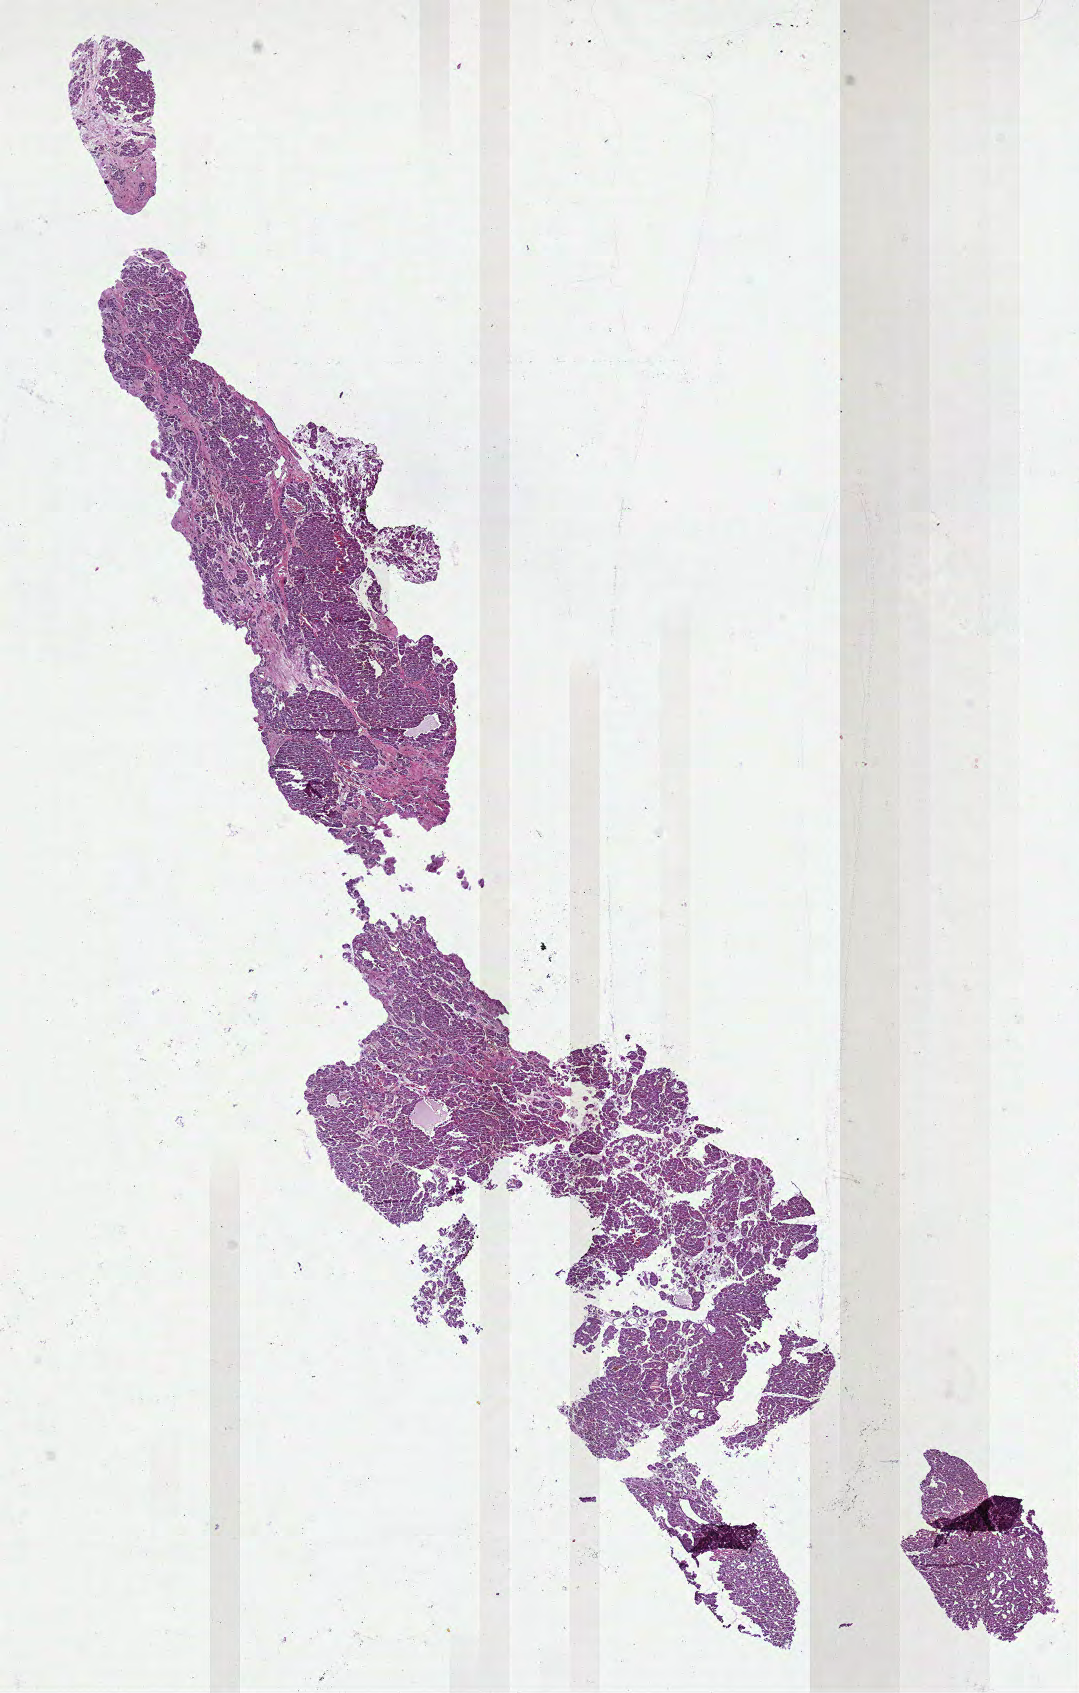
Digitized H&E tissue section (whole slide) — shown as a low-resolution overview of the whole scanned area (about 8.7 x 13.7 mm, slide scanned at 40x); formalin-fixed paraffin-embedded (FFPE) diagnostic section; kidney, primary tumour sample. Male patient; age at initial diagnosis 74 years.
- diagnosis: Renal cell carcinoma, chromophobe type
- AJCC pathologic stage: I (7th edition)